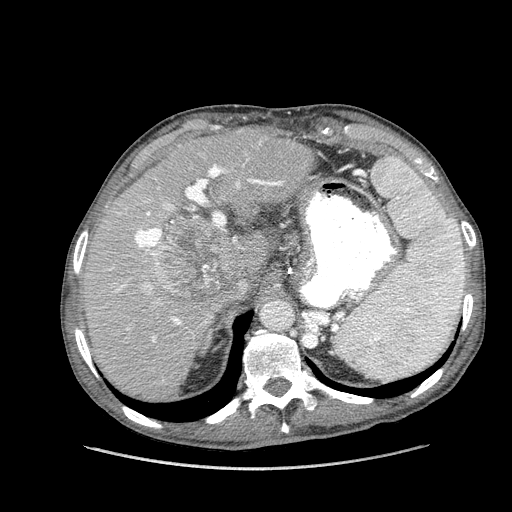
Contrast-enhanced abdominal CT (liver protocol), one axial slice. Slice 103 of 162 in the series (ordered by position). Reconstruction kernel STANDARD. Soft-tissue window (W 400 / L 40 HU). 2.5 mm slice thickness. 512 × 512 image matrix, field of view 400 × 400 mm. From the clinical record (not read from this slice): diagnosis: hepatocellular carcinoma (patient treated with transarterial chemoembolisation; whether this scan precedes or follows treatment is not stated here); TNM stage (as recorded): Stage-IIIA; Child-Pugh class: A; tumour nodularity: multinodular.
Annotated regions visible in this slice (semi-automatic segmentation, software-assisted and operator-edited):
- liver parenchyma outside the tumour (the mass and vessels are separate outlines, so this box may not span the whole liver): box from (x=82, y=128) to (x=314, y=400) px
- mass: (x=152, y=212)–(x=238, y=303)
- liver vessels: (x=109, y=164)–(x=283, y=343)